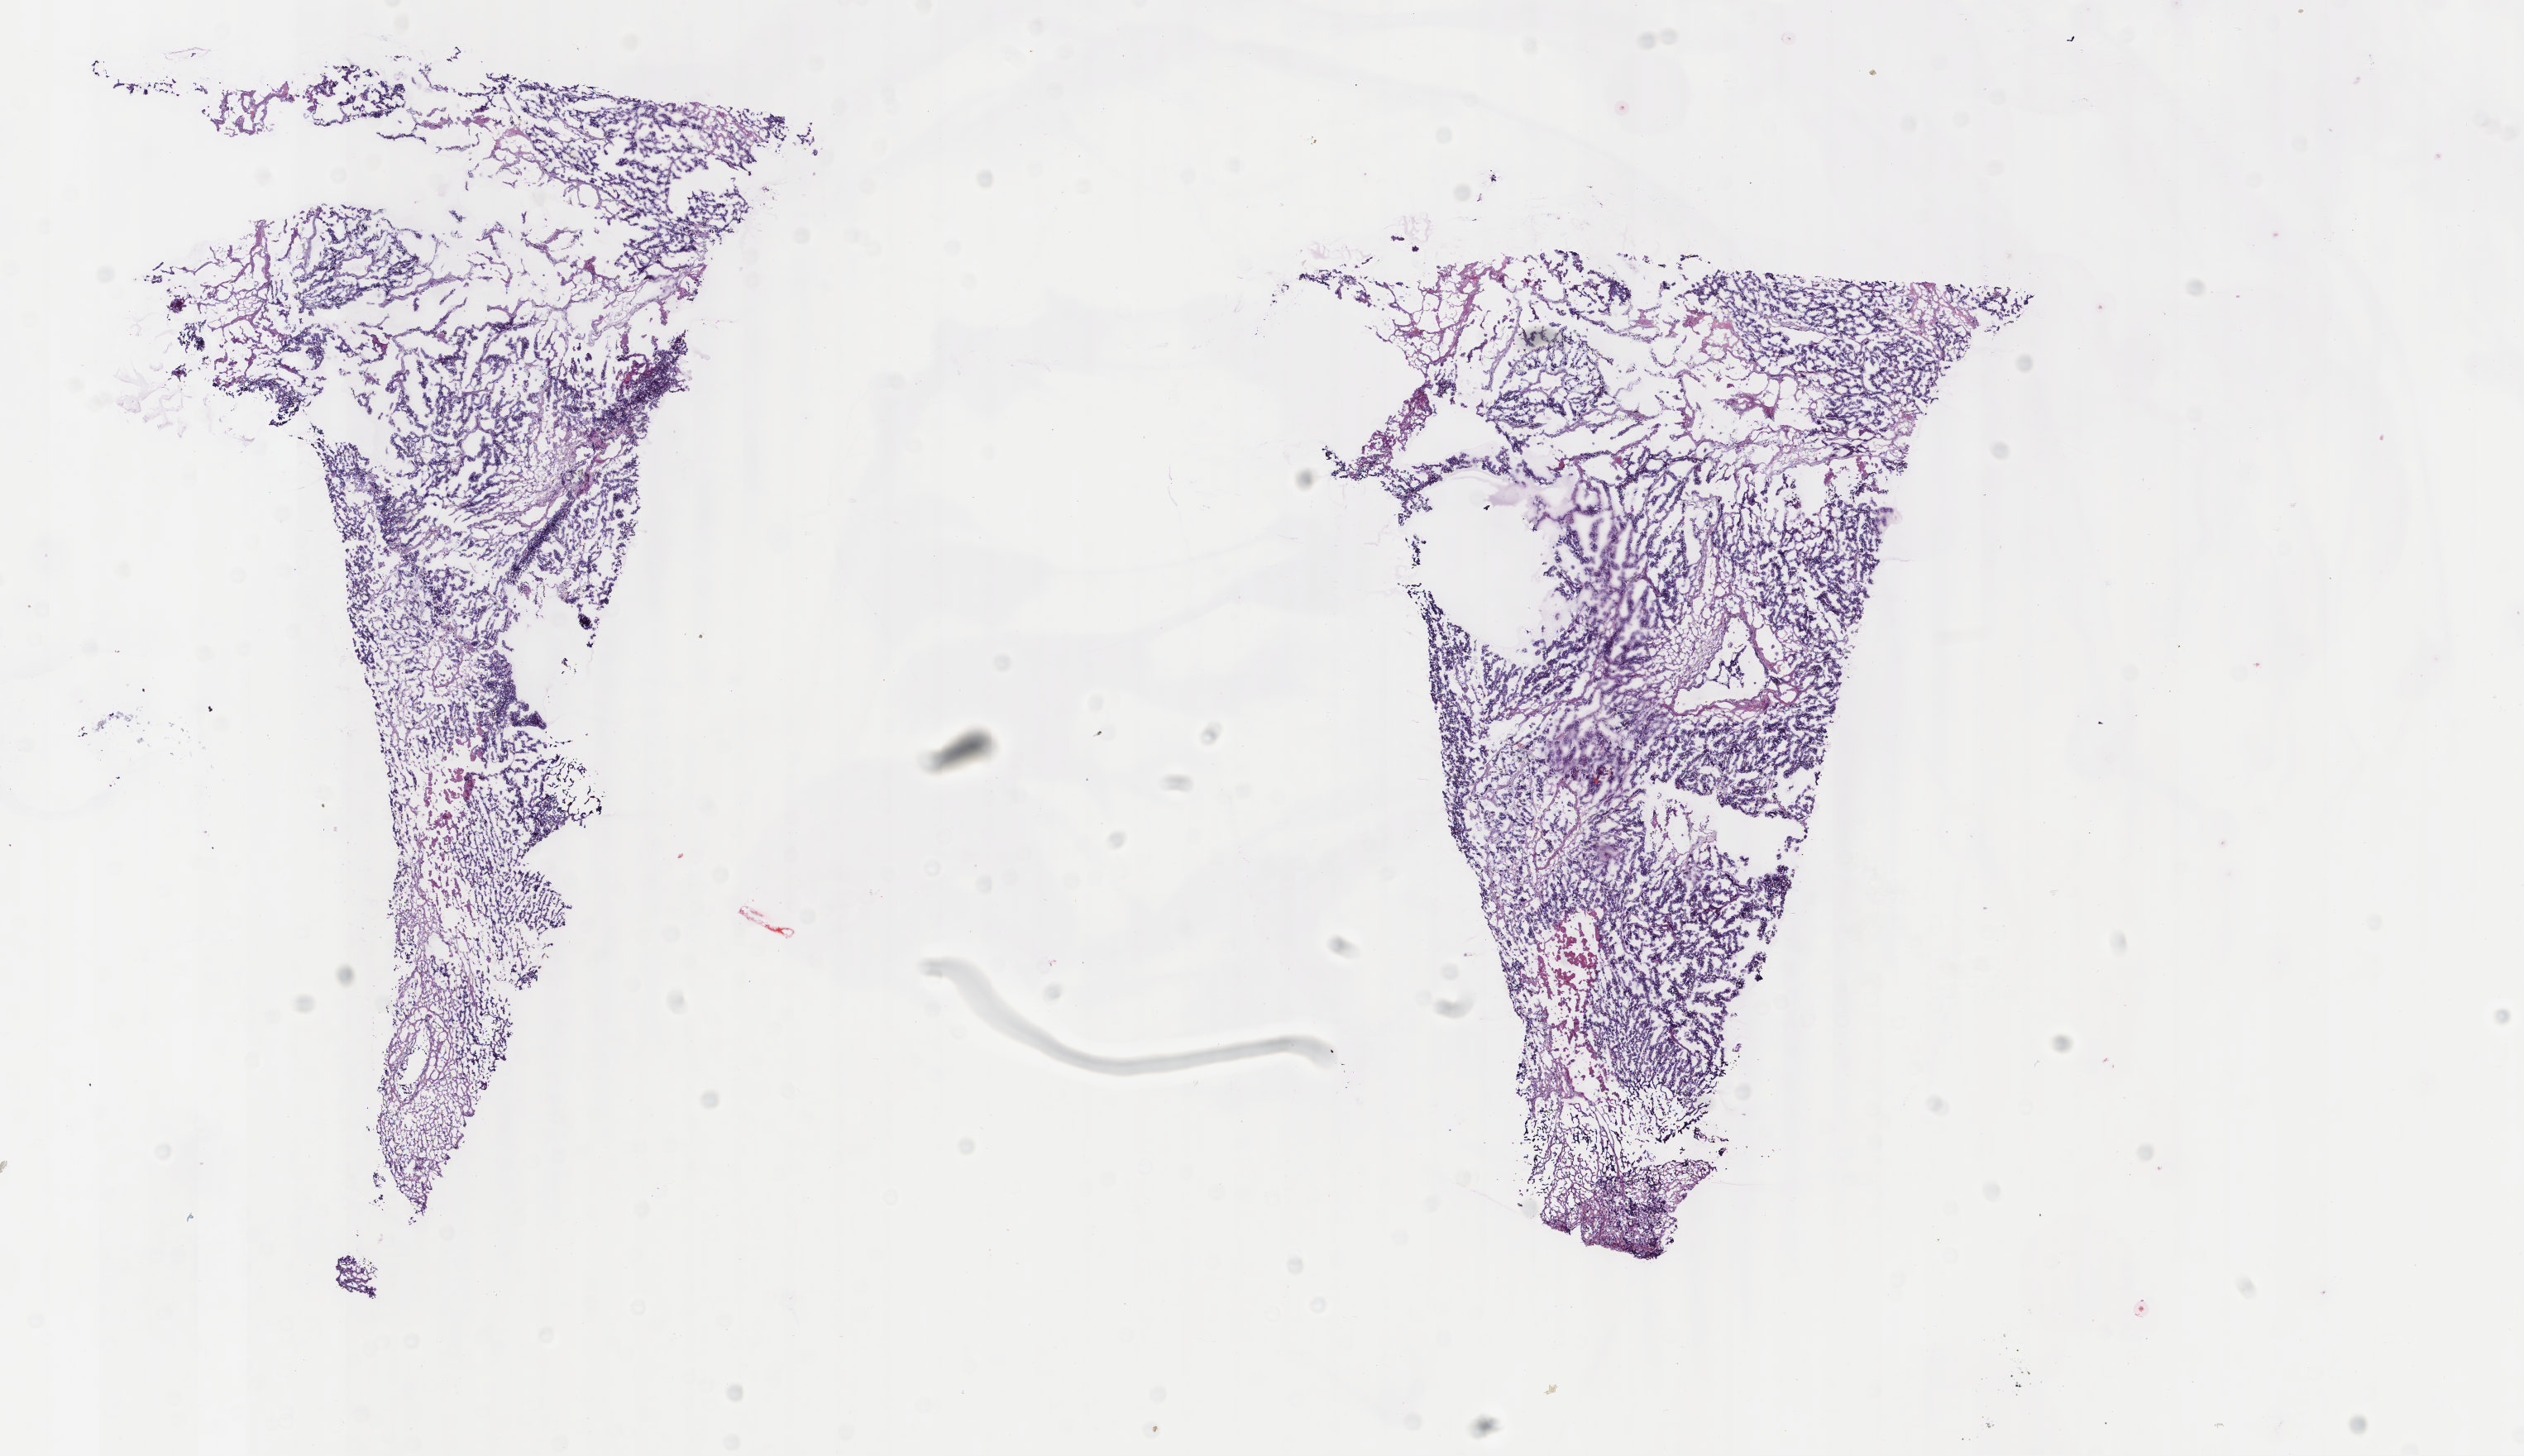
H&E-stained whole-slide image — a low-resolution overview of the entire scanned area, about 12.1 x 7.0 mm (from a 40x scan); frozen section from the bottom of the tissue portion; uterus, primary tumour sample. Patient: female, age at initial diagnosis 64 years. Histologic grade: G3 (poorly differentiated). Pathologist review of this section (percent, as recorded): tumour cells 70%, tumour nuclei 94%, normal cells 8%, stromal cells 2%, necrosis 20%. Infiltration values recorded for this section: lymphocyte infiltration 0%, monocyte infiltration 0%, neutrophil infiltration 0%.
• lymph nodes positive (case pathology): 1 of 22 examined
• diagnosis: Endometrioid adenocarcinoma, NOS (endometrium)
• FIGO stage: IIIC1